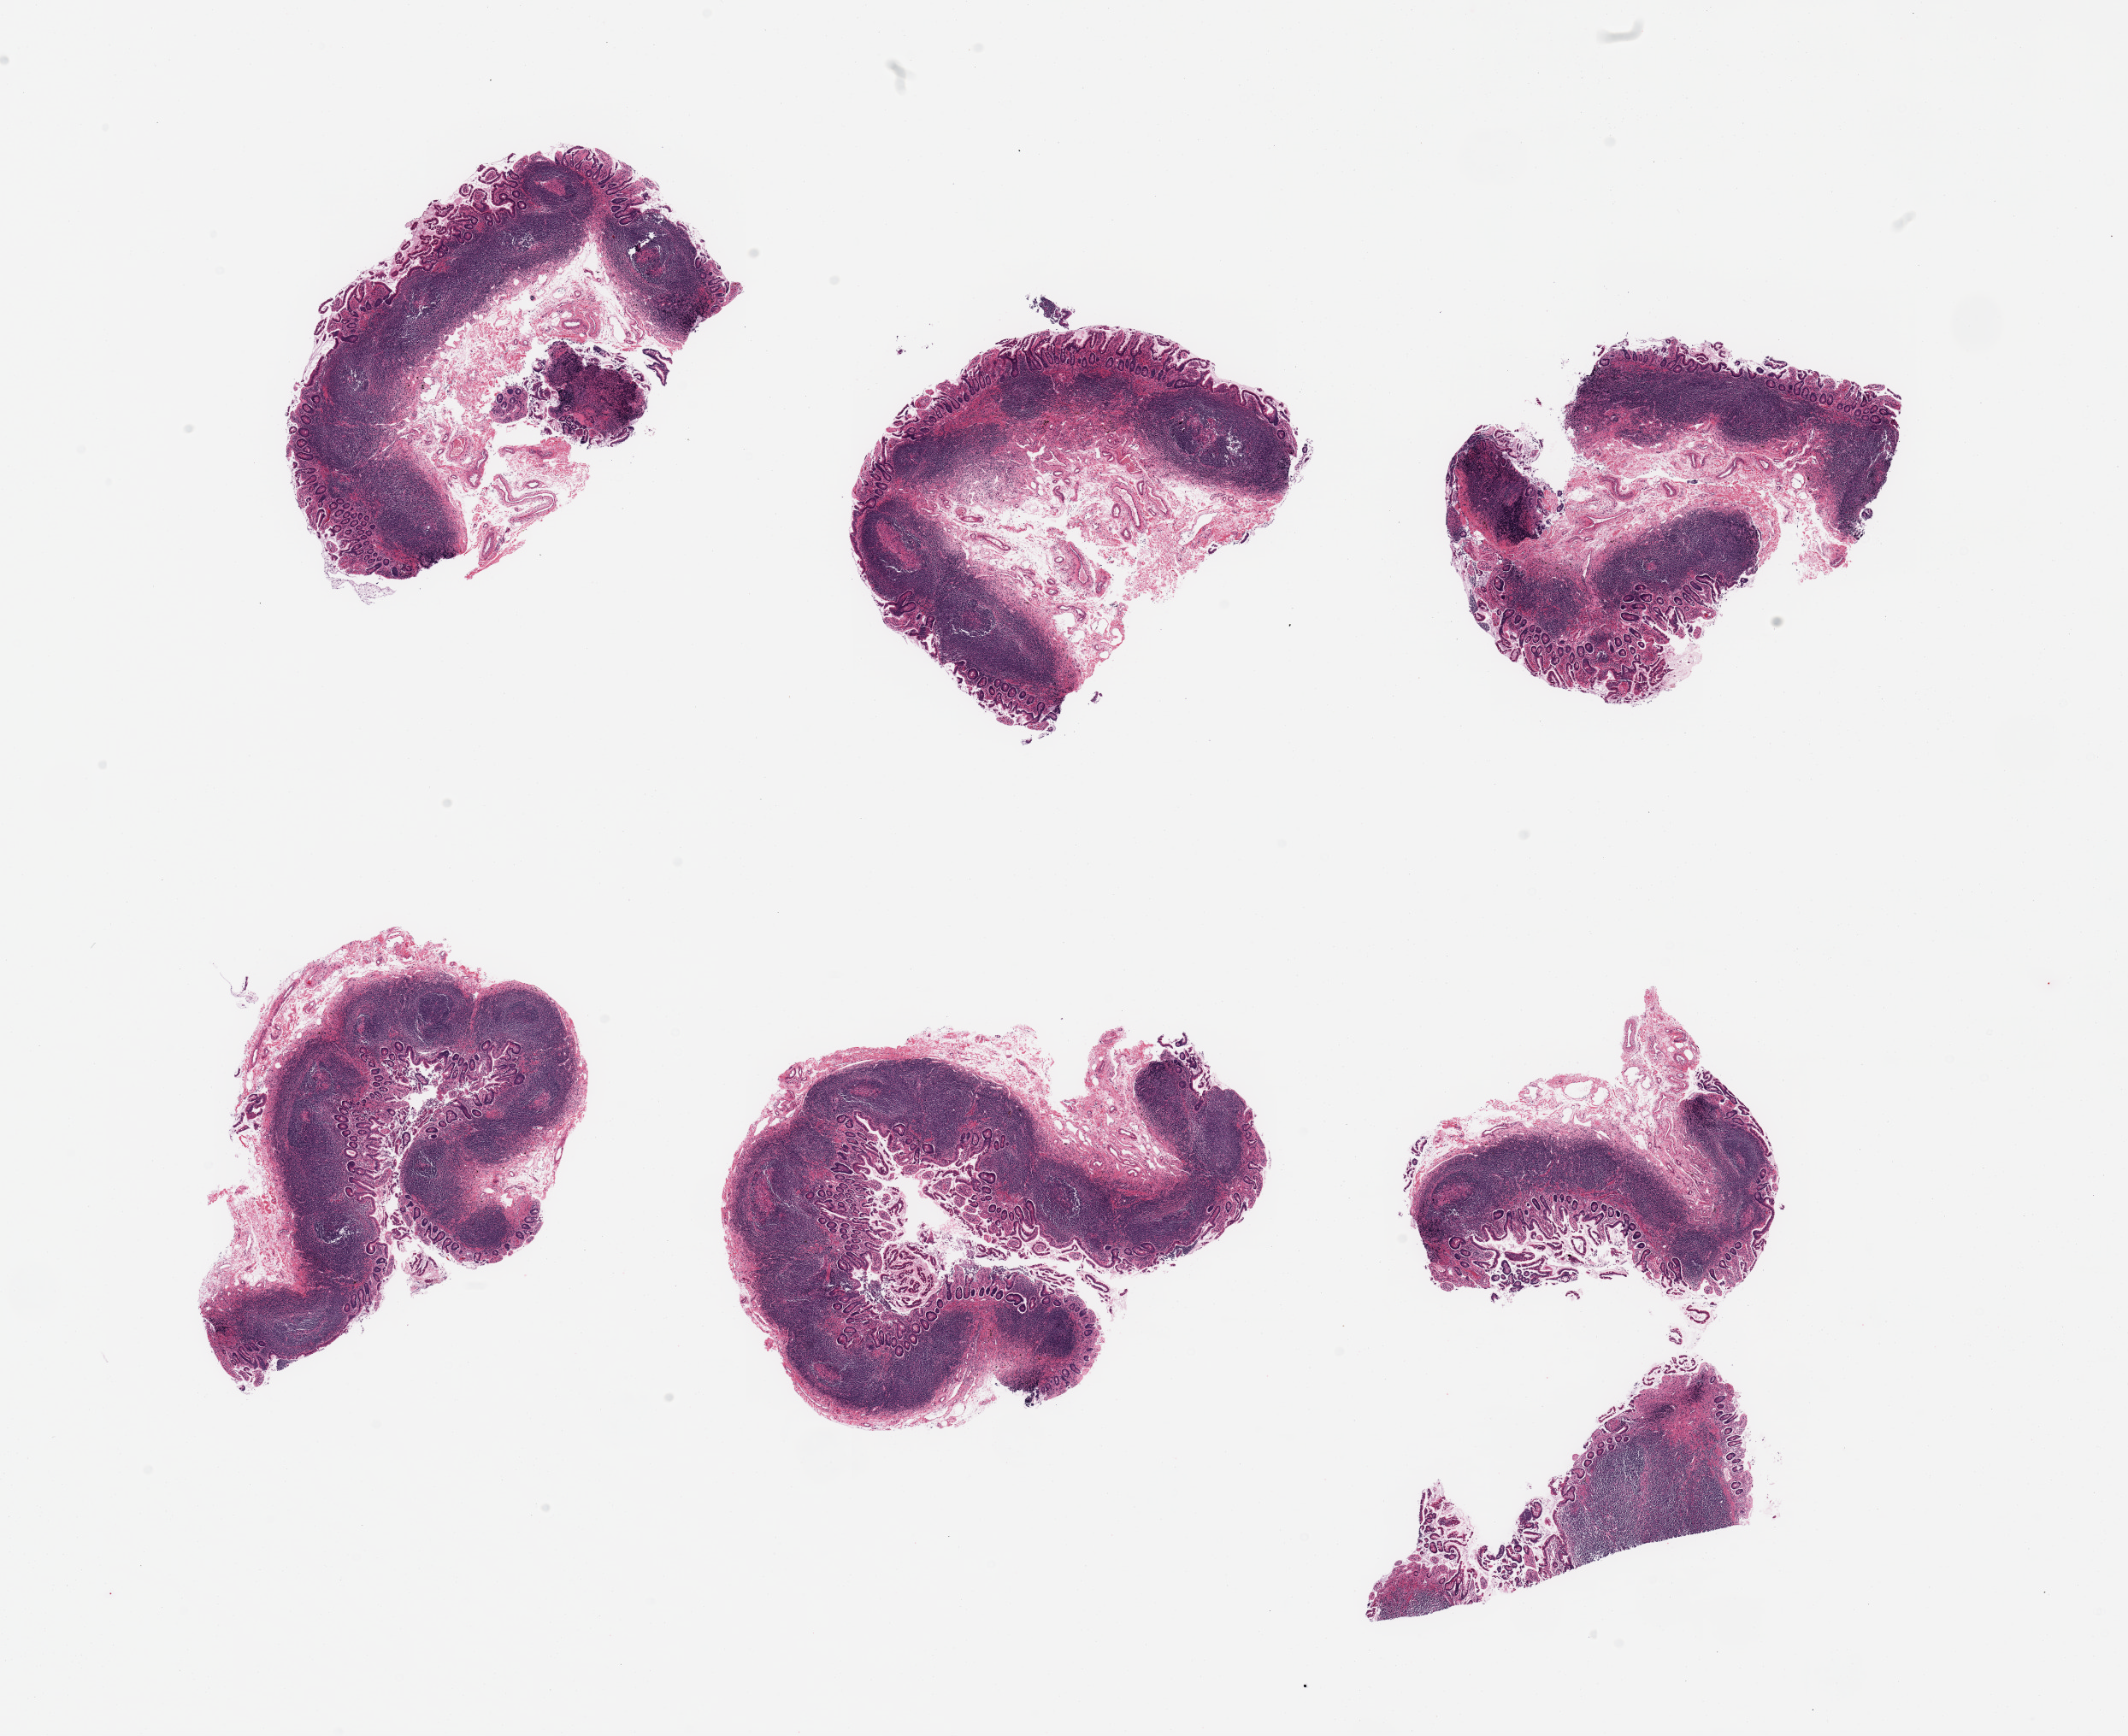
Whole-slide image, hematoxylin and eosin (H&E) stain, brightfield, whole scanned area (about 19.7 x 16.1 mm) shown as a low-resolution overview. PAXgene-fixed paraffin-embedded (PFPE) section. Section of ileum (target tissue). Tissue donor sample. Female donor.
Review note (as recorded): 6 pieces; lymphoid-rich mucosa on all pieces comprise 80% of area; glands partially sloughed.